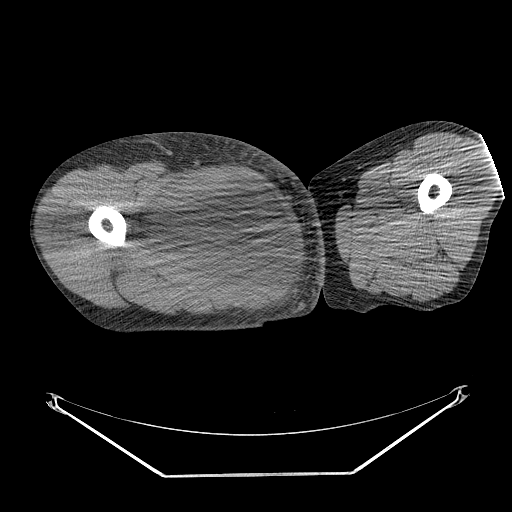
CT of an extremity soft-tissue mass (from a PET/CT study), one axial slice. Position 252 of 311 along the scan axis. Soft-tissue window (W 400 / L 40 HU). 3.75 mm slice thickness. 512 × 512 image matrix, field of view 500 × 500 mm. Male patient. From the clinical record (not read from this slice): histological type: undifferentiated - pleiomorphic; grade: high; site of the primary tumour: right thigh.
Outlined on this slice (expert contour drawn on MRI and transferred to this co-registered scan by the dataset authors):
- gross tumour volume including surrounding oedema: bounding box (x1, y1, x2, y2) in pixels: (137, 171, 259, 268)
- gross tumour volume (mass): (155, 174, 257, 268)